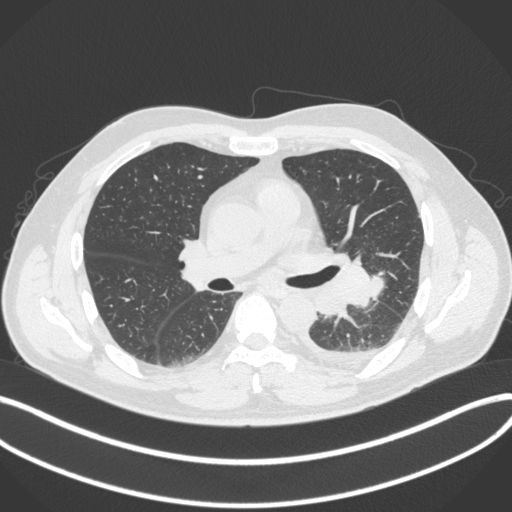
Chest CT, one axial slice. Slice 205 of 350 in the series (ordered by position). Reconstruction kernel B31f. Lung window (W 1500 / L -600 HU). 1 mm slice thickness. 512 × 512 image matrix. Male patient, age 58 years. Case-level facts recorded for this patient, not image findings: clinical TNM (as recorded): T3 N1 M1b; histopathological grade: G3.
Annotated regions visible in this slice (bounding box drawn by a radiologist):
- lung tumour (recorded histology: small cell carcinoma): bounding box (x1, y1, x2, y2) in pixels: (306, 261, 381, 316)